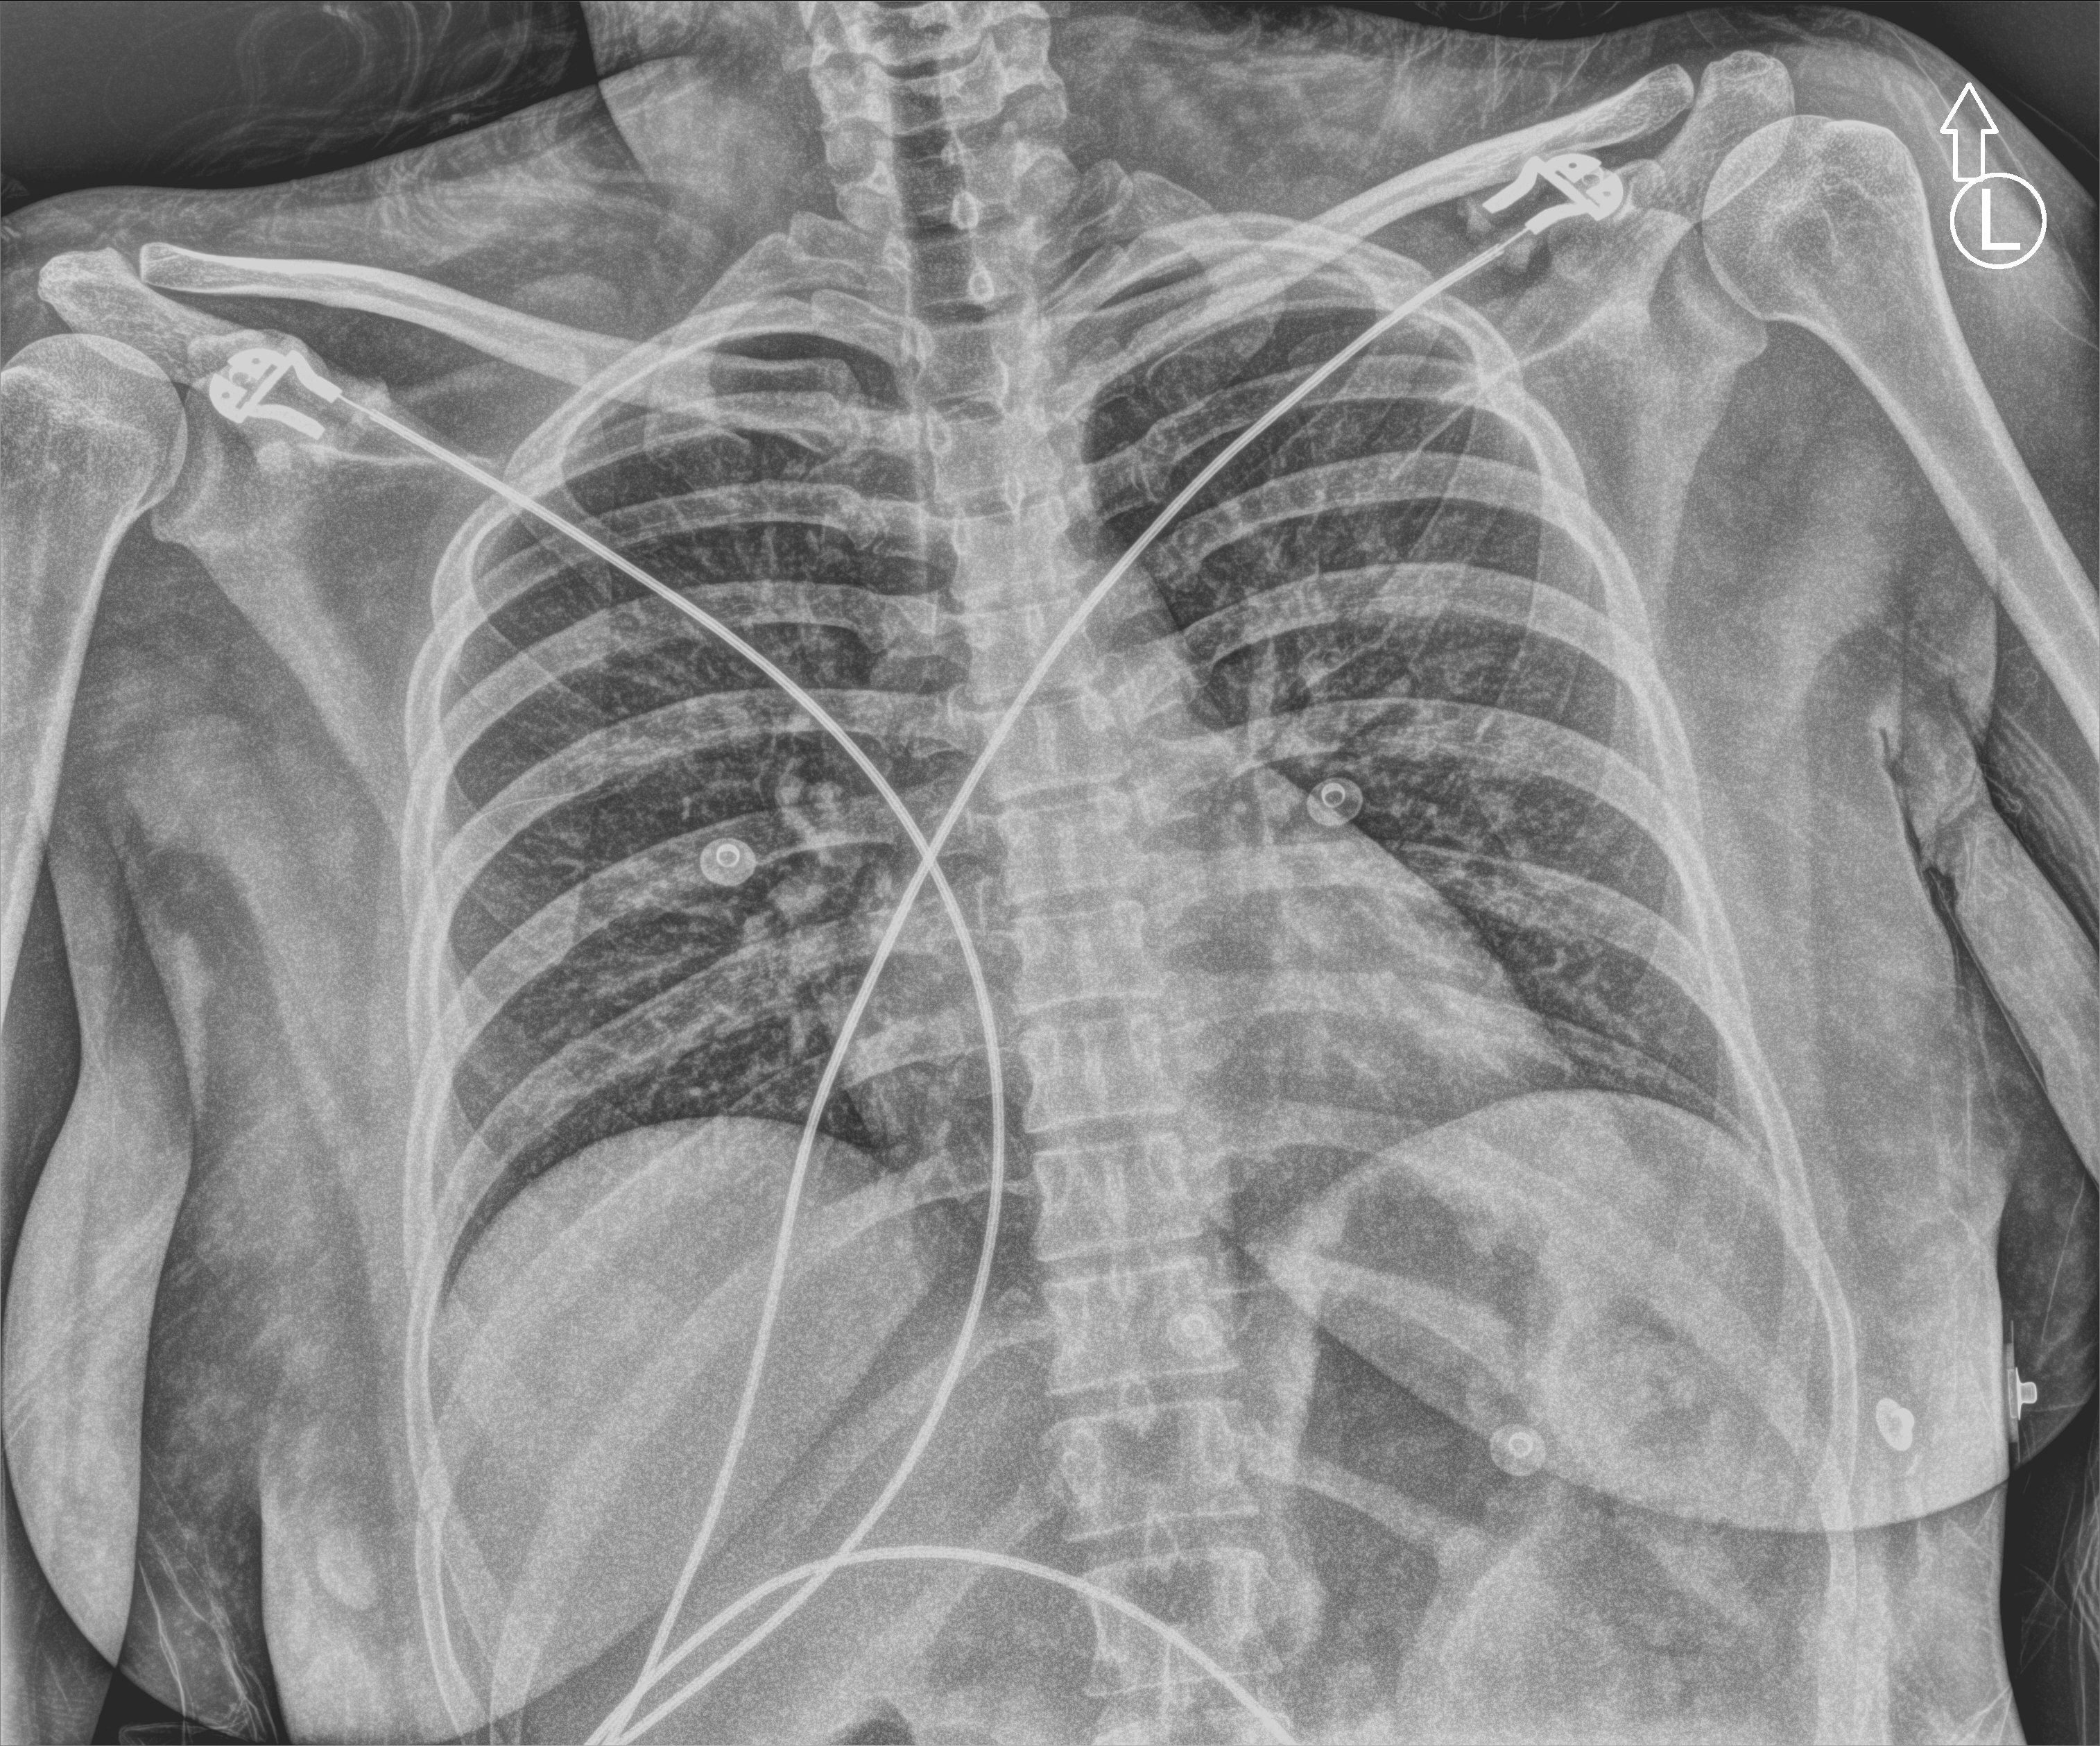
Portable chest radiograph, anteroposterior (AP) projection. Female patient hospitalised with COVID-19, age 18–59 years.
Hospital-stay facts (about this admission, not read from this image; timing relative to this image not recorded): admitted to intensive care during this hospital stay: no.